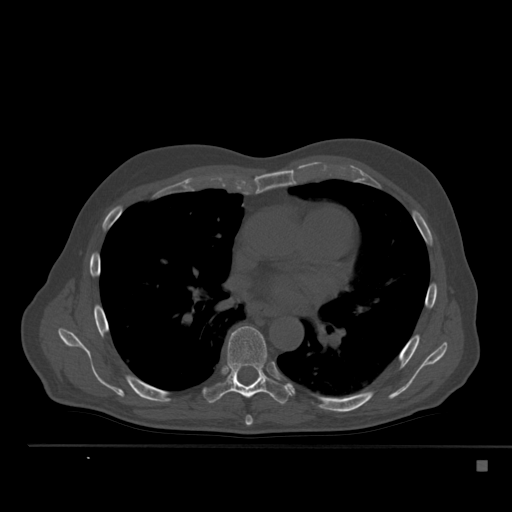
CT including the spine, one axial slice; position 330 of 517 along the scan axis; reconstruction kernel Br40s; 120 kVp; bone window (W 1800 / L 400 HU); 1.5 mm slice thickness; 512 × 512 image matrix, field of view 408 × 408 mm. Male patient, age 70 years. From the clinical record (not read from this slice): primary cancer: renal; vertebrae with lytic lesions (as recorded): T4, T6, T10, T12, L3, L4, L5.
Structures marked on this image (semi-automatically segmented with operator editing):
- T6 vertebra: bounding box <245,416,253,426> (left, top, right, bottom; pixels)
- T7 vertebra: <202,326,291,404>